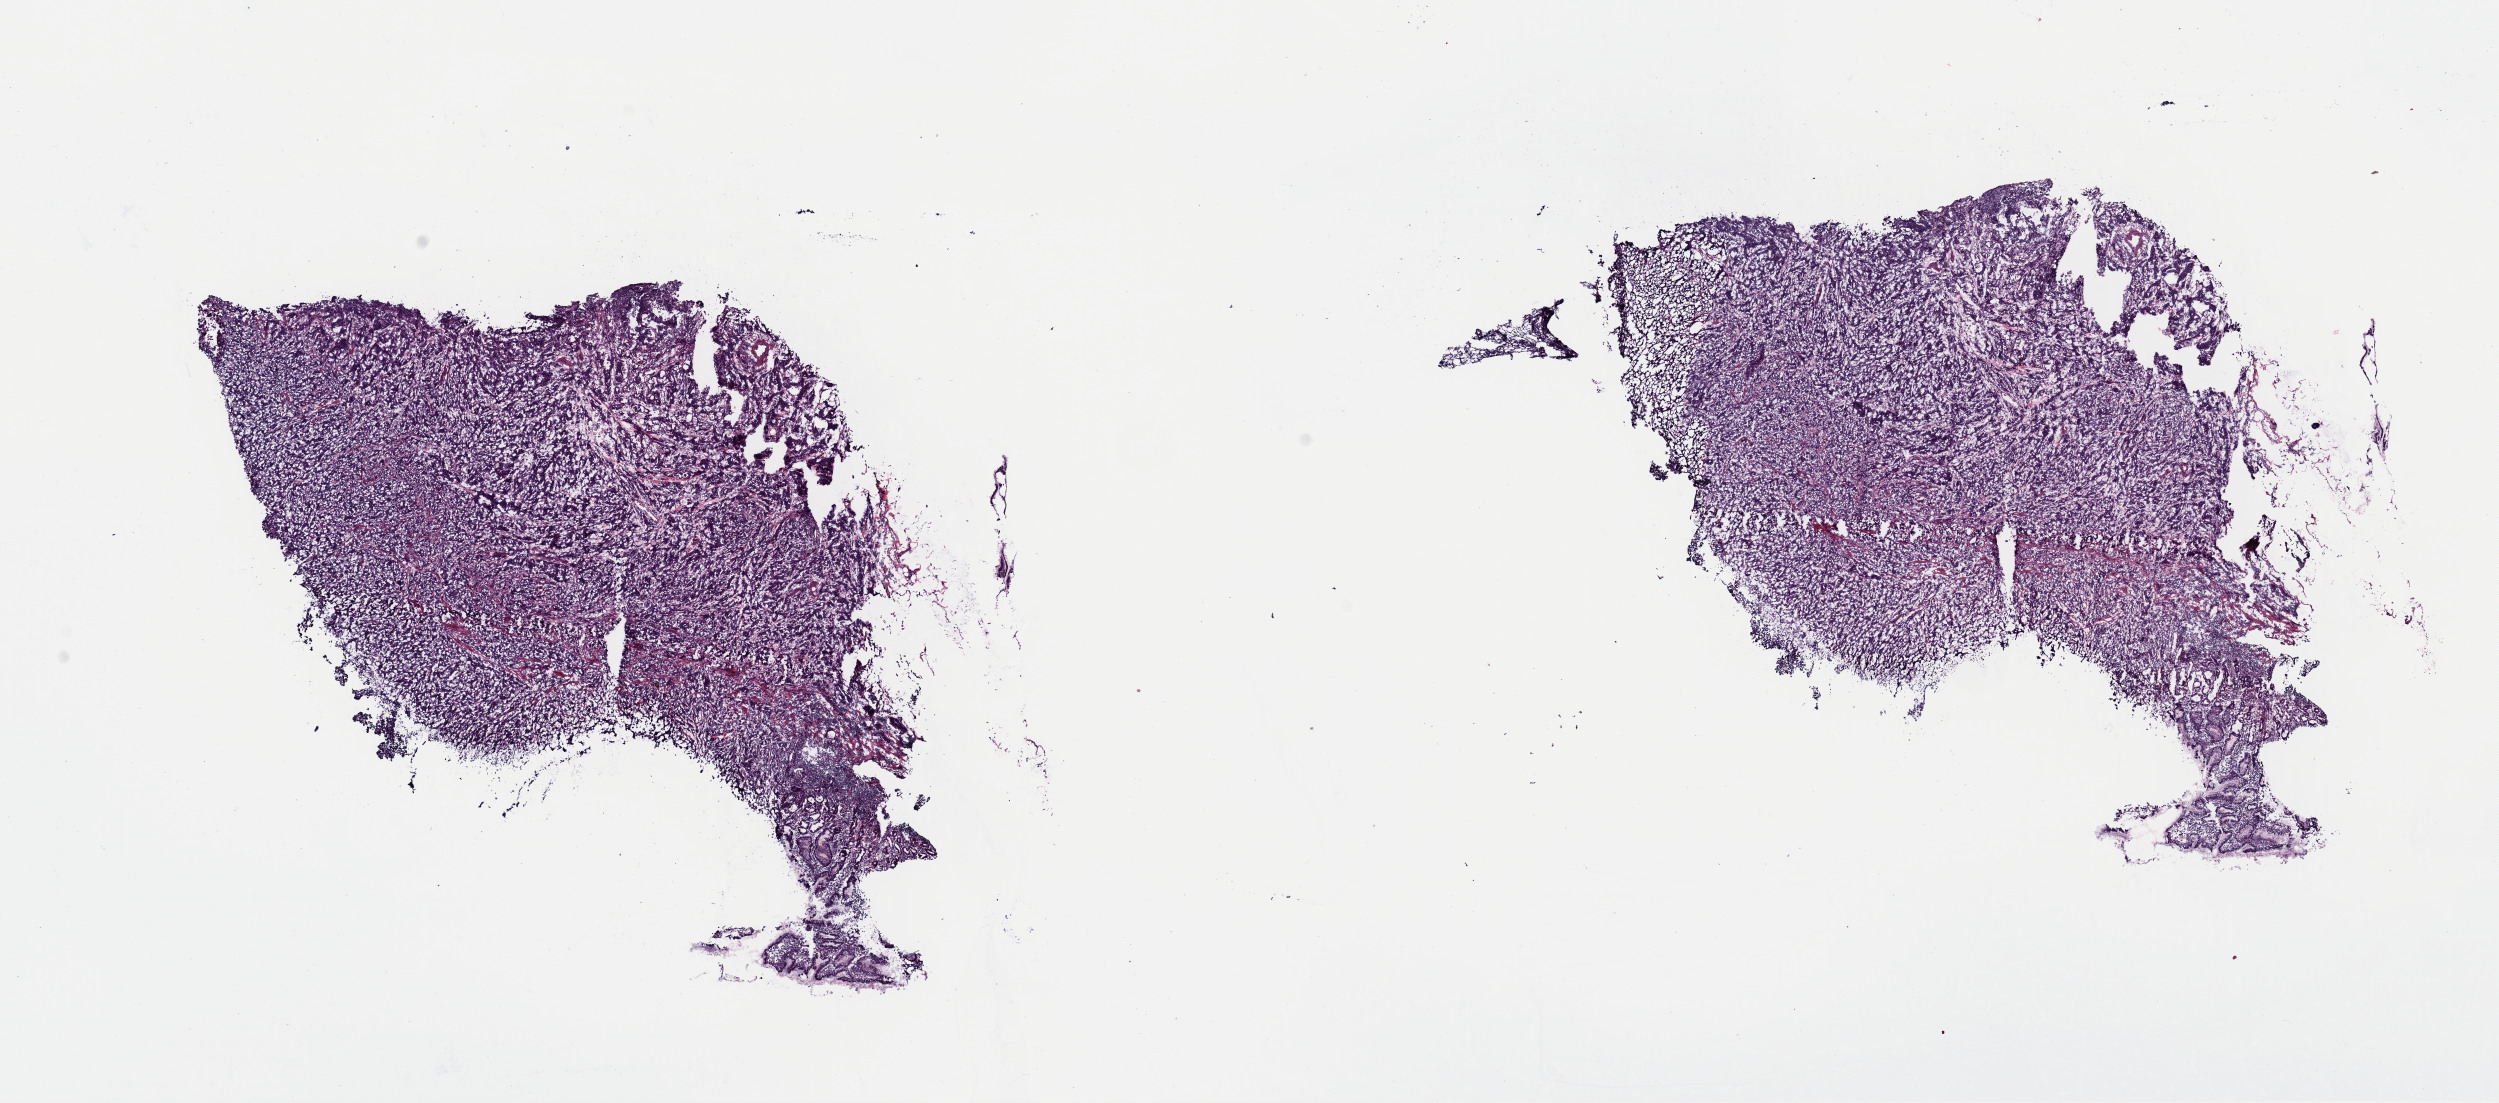
Digitized Hematoxylin and eosin (H&E) stained tissue section (whole slide), whole scanned area (about 19.7 x 8.7 mm, slide scanned at 40x) shown as a low-resolution overview. Frozen section from the top of the tissue portion. Sample: primary tumour, stomach. Female patient; age at initial diagnosis 70 years. Histologic grade: G3 (poorly differentiated). Pathologist review of this section (percent, as recorded): tumour cells 61%, tumour nuclei 80%, normal cells 7%, stromal cells 20%, necrosis 12%. Inflammatory infiltration, as recorded: lymphocyte infiltration 7%, monocyte infiltration 0%, neutrophil infiltration 0%.
TNM: T4b N2 M0. AJCC pathologic stage: IIIC (7th edition). Pathologic diagnosis: Carcinoma, diffuse type. Lymph nodes positive (case pathology): 6 of 71 examined.